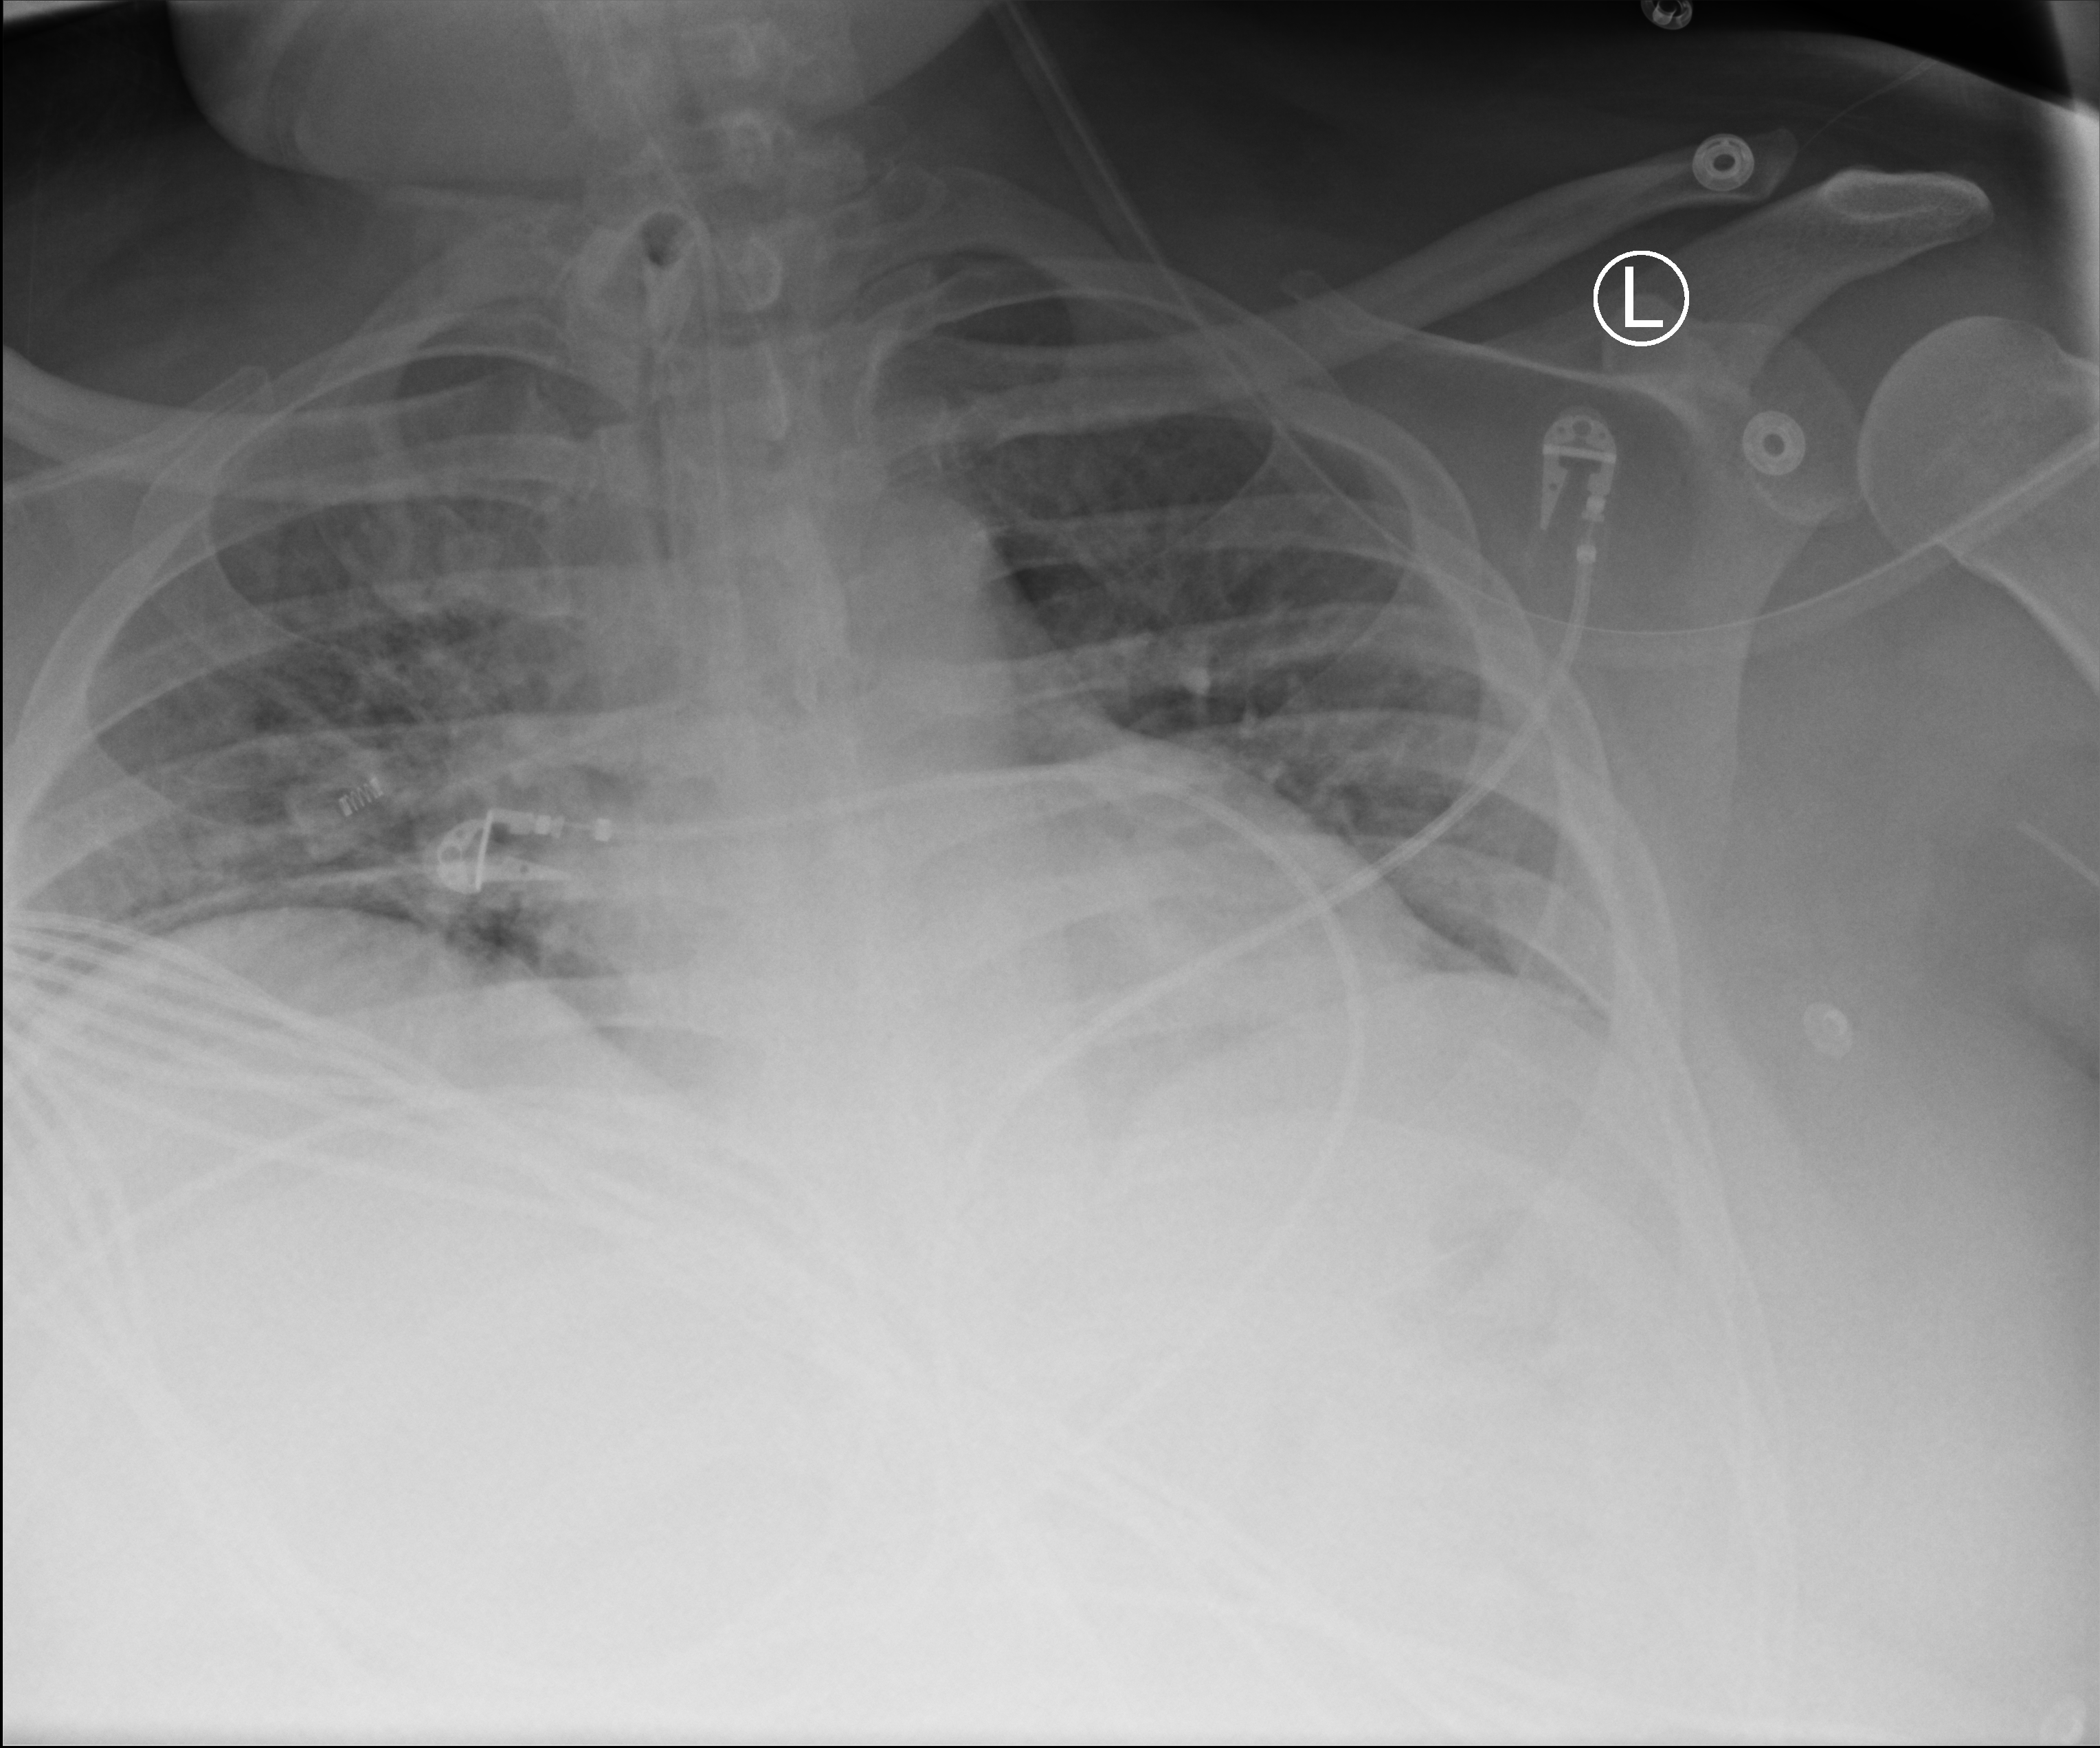
Bedside chest radiograph (computed radiography); anteroposterior (AP) projection. Patient hospitalised with COVID-19; male, aged 18–59 years.
Hospital-stay facts (about this admission, not read from this image; timing relative to this image not recorded): mechanically ventilated during this hospital stay: yes; admitted to intensive care during this hospital stay: yes.